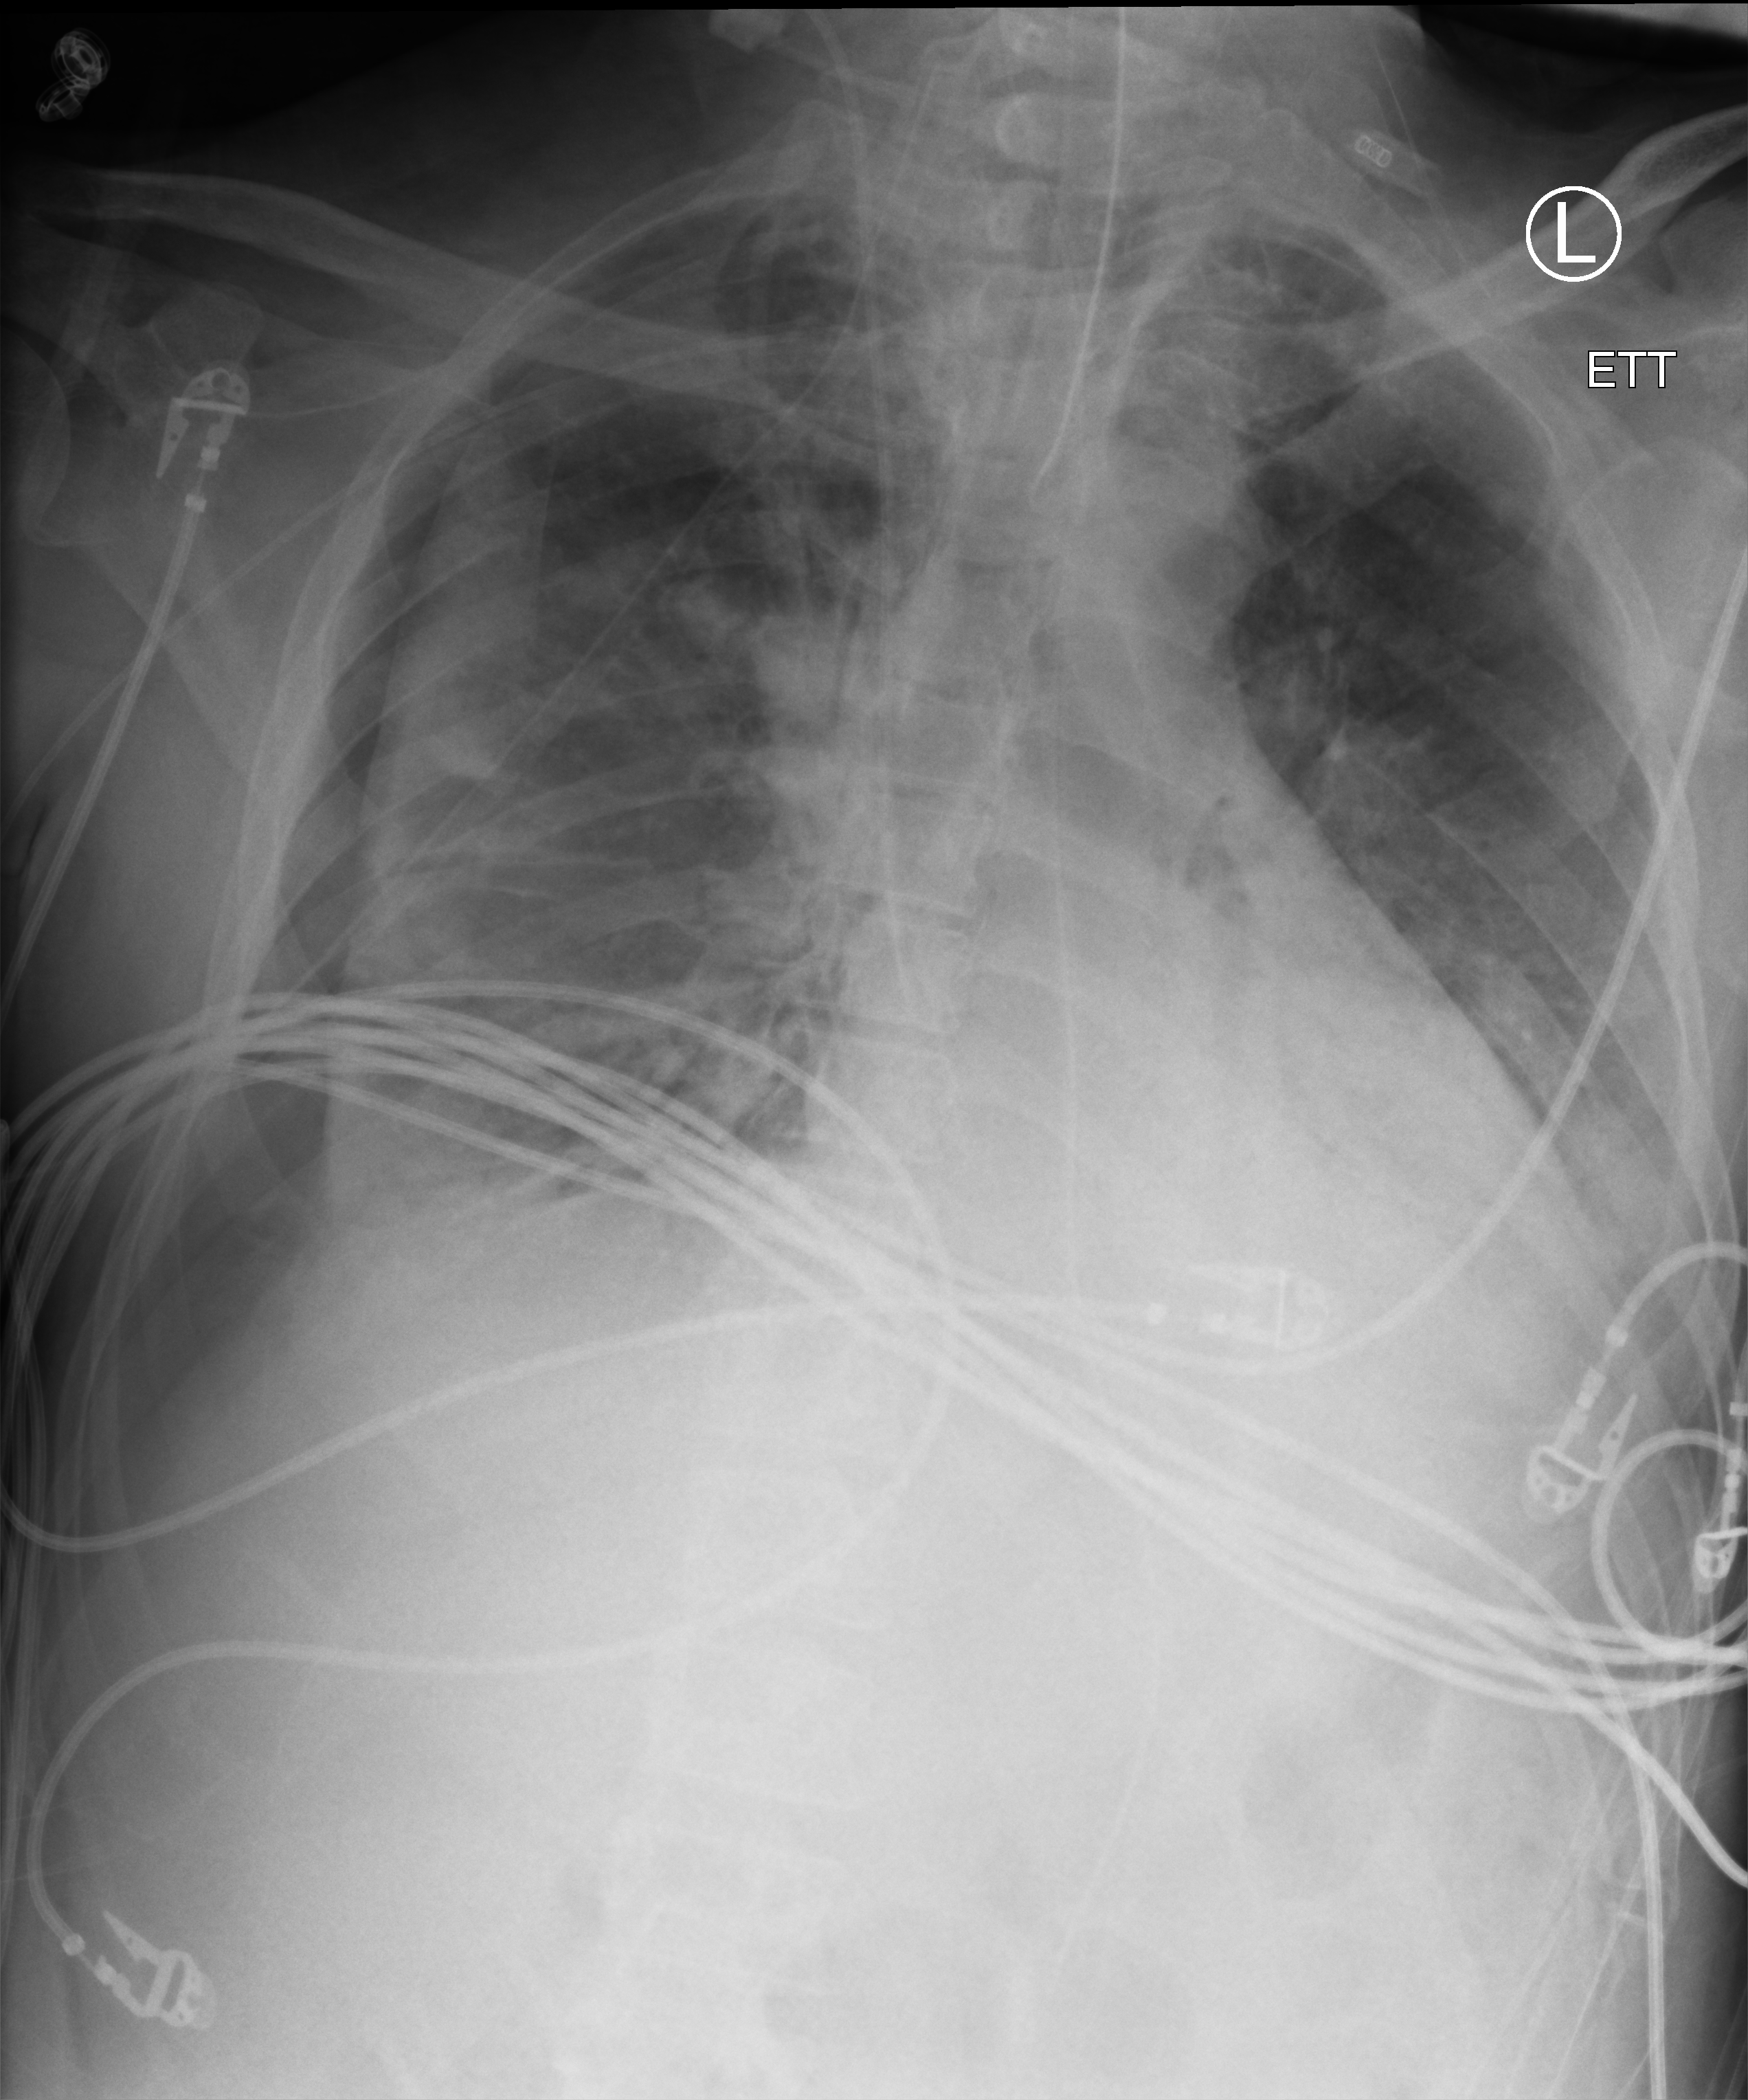
Portable chest radiograph; anteroposterior (AP) projection. Male patient hospitalised with COVID-19, age 18–59 years.
From the hospital-stay record, not from the radiograph (when in the stay this image was taken is not recorded): mechanically ventilated during this hospital stay: yes.